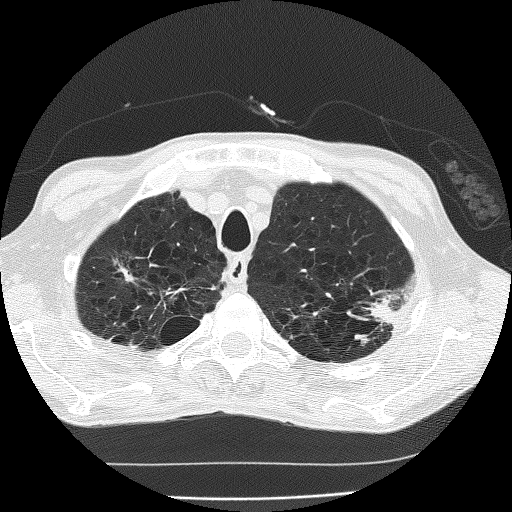
Low-dose screening chest CT, one axial slice. Slice 156 of 185 in the series (ordered by position). Reconstruction kernel FC51. 120 kVp. Lung window (W 1500 / L -600 HU). 2 mm slice thickness. 512 × 512 image matrix, field of view 320 × 320 mm.
Annotated regions visible in this slice (manually delineated by an expert):
- lesion 1 (tumor, upper lobe of left lung): bounding box [x1, y1, x2, y2] px = [368, 297, 400, 327]